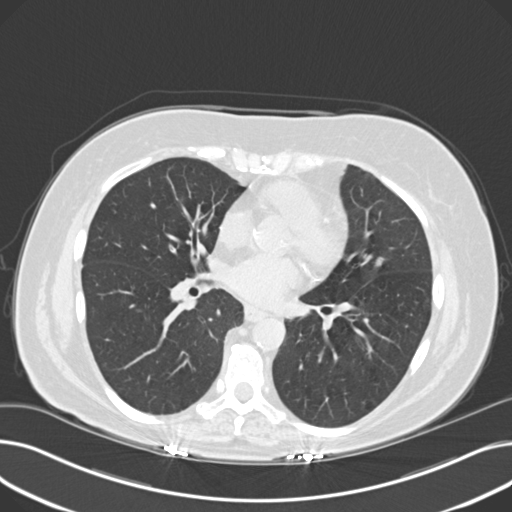
Axial slice from a low-dose chest CT screening exam. Third screening round (two years after baseline). Lung window (W 1500 / L -600 HU). Female, age 60 years at enrolment. Current smoker at enrolment.
- Expert reader's lesion annotation, bounding box [x1, y1, x2, y2] px = [362, 252, 396, 282].
- The screening reader recorded 8 non-calcified nodules or masses ≥4 mm on this exam (right upper lobe, lingula, lingula, right middle lobe, right lower lobe, left lower lobe, left lower lobe, left lower lobe); which of them this box marks is not recorded.